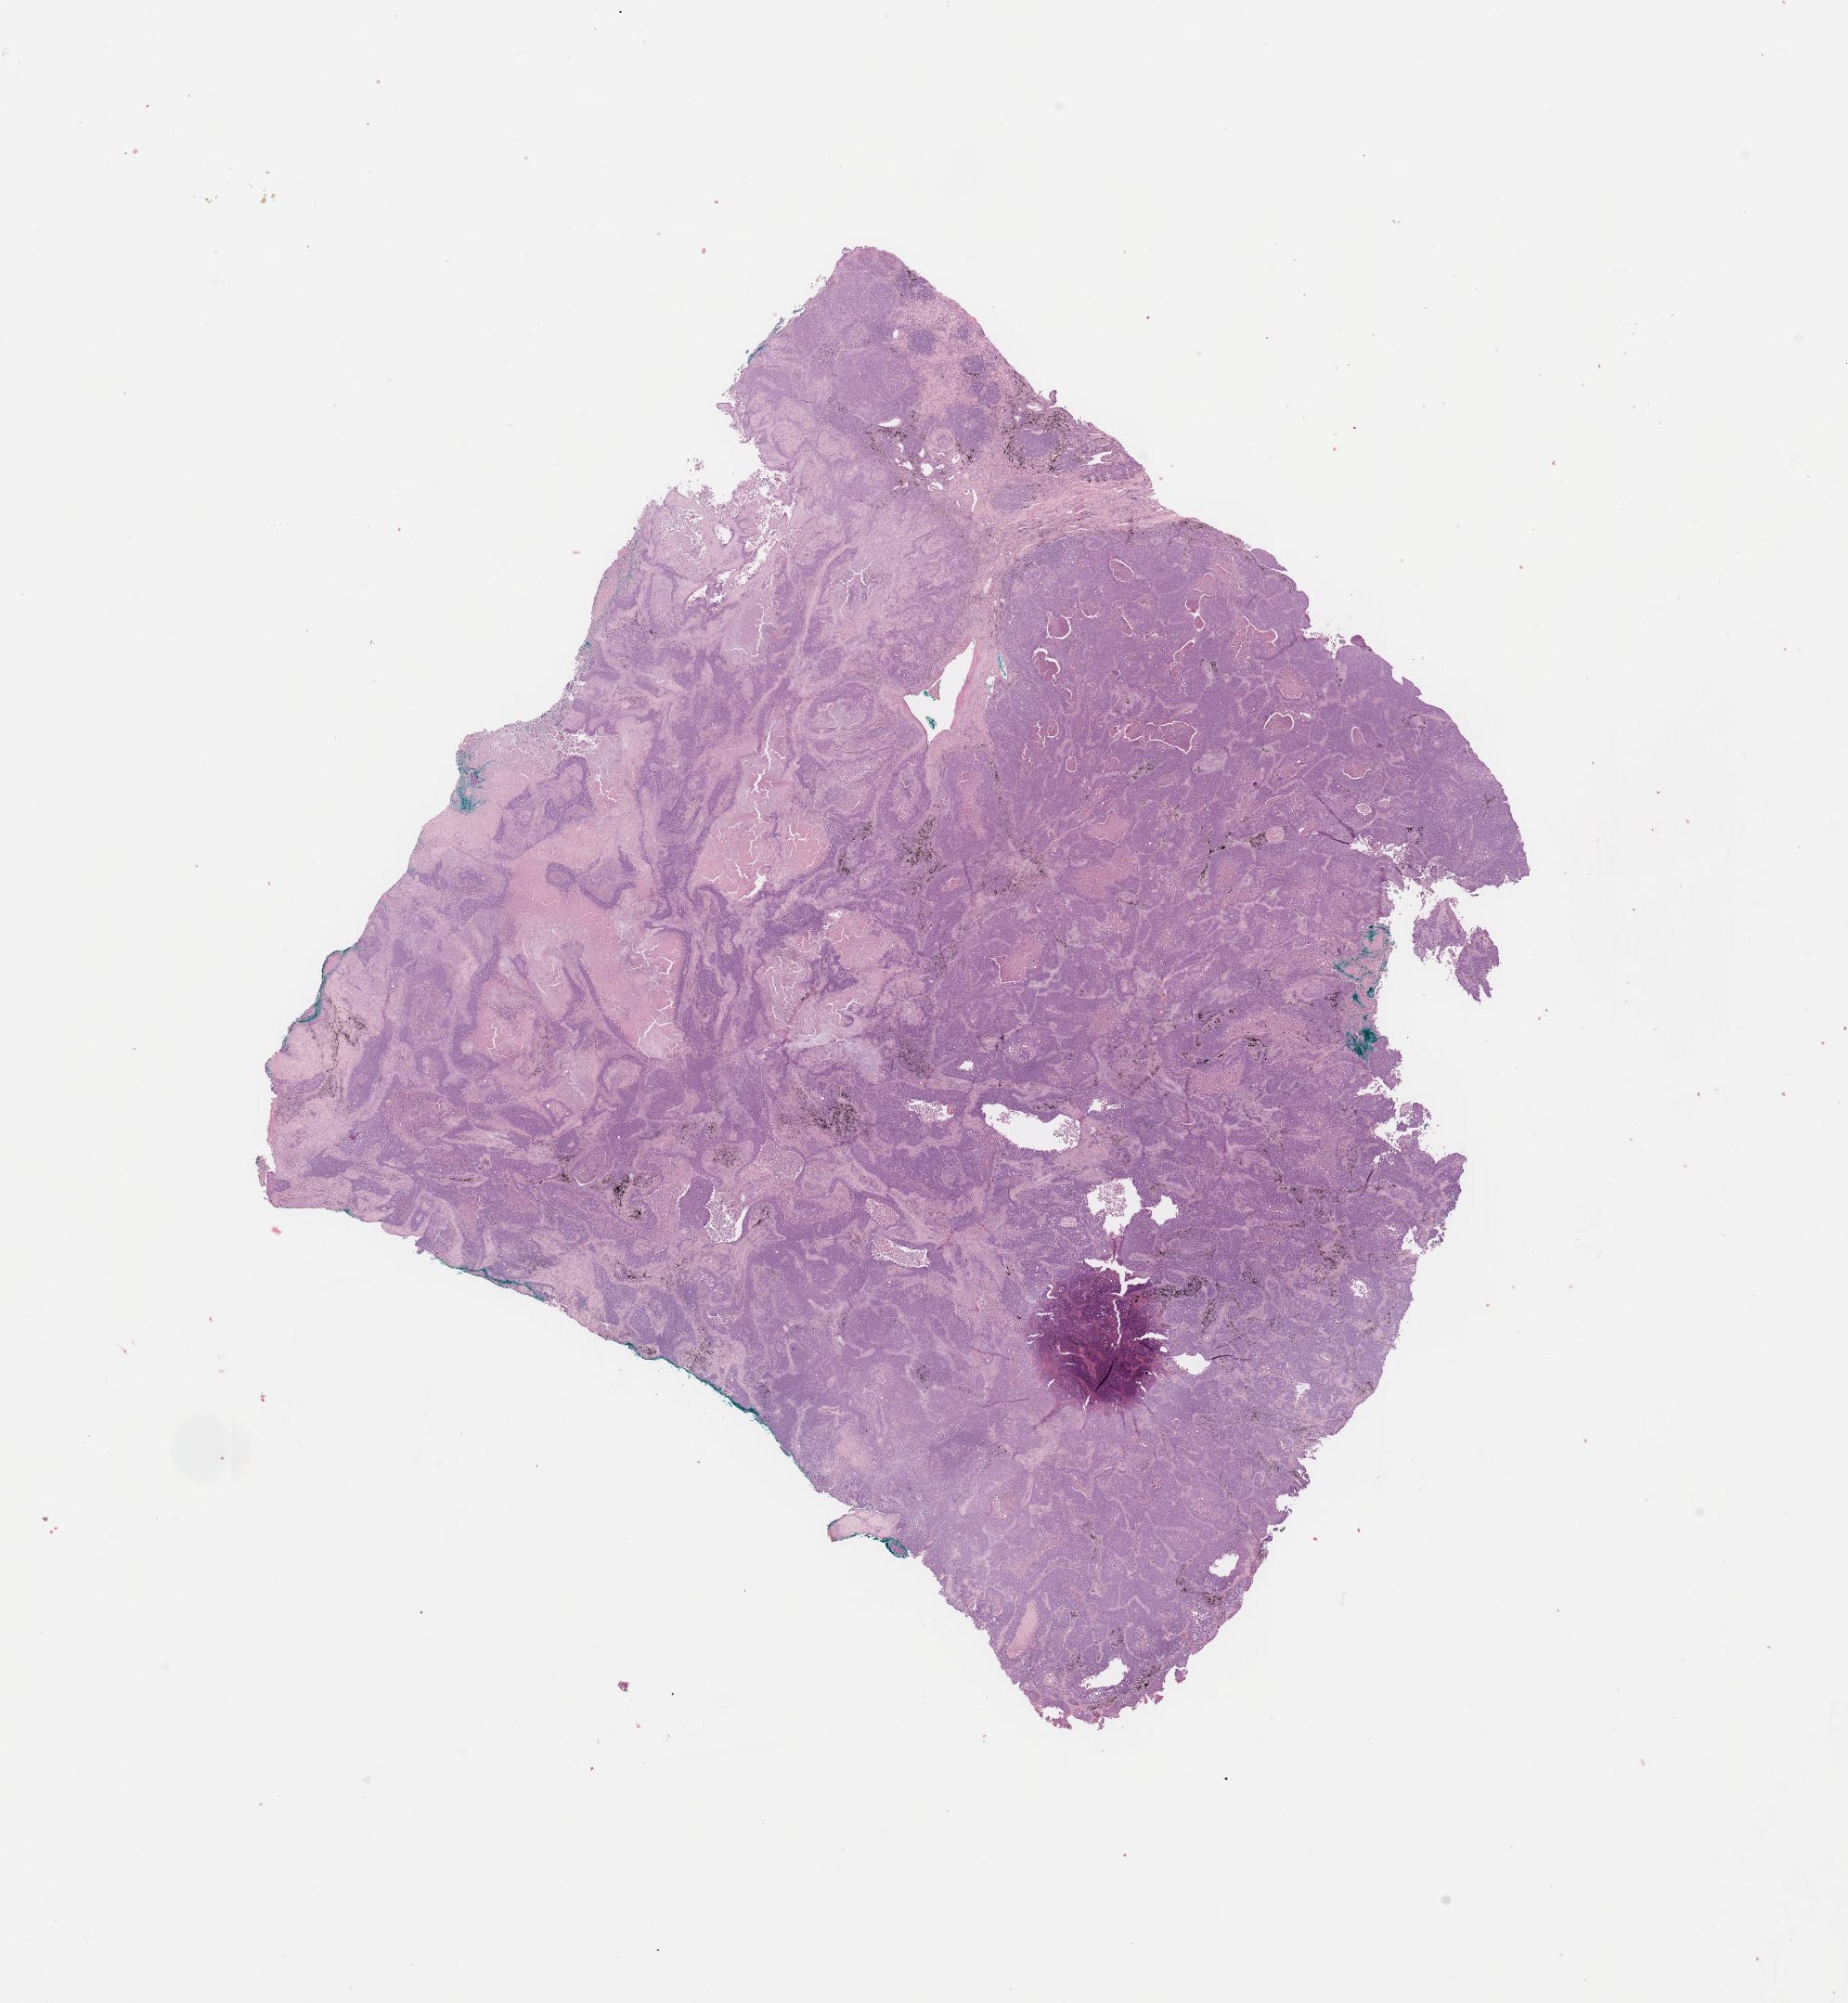
Digitized H&E-stained tissue section (whole slide) — shown as a low-resolution overview of the whole scanned area (about 15.8 x 17.1 mm, slide scanned at 20x), tumour tissue sample, lung. Male, 75 y/o.
Diagnosis: Squamous cell carcinoma, NOS.